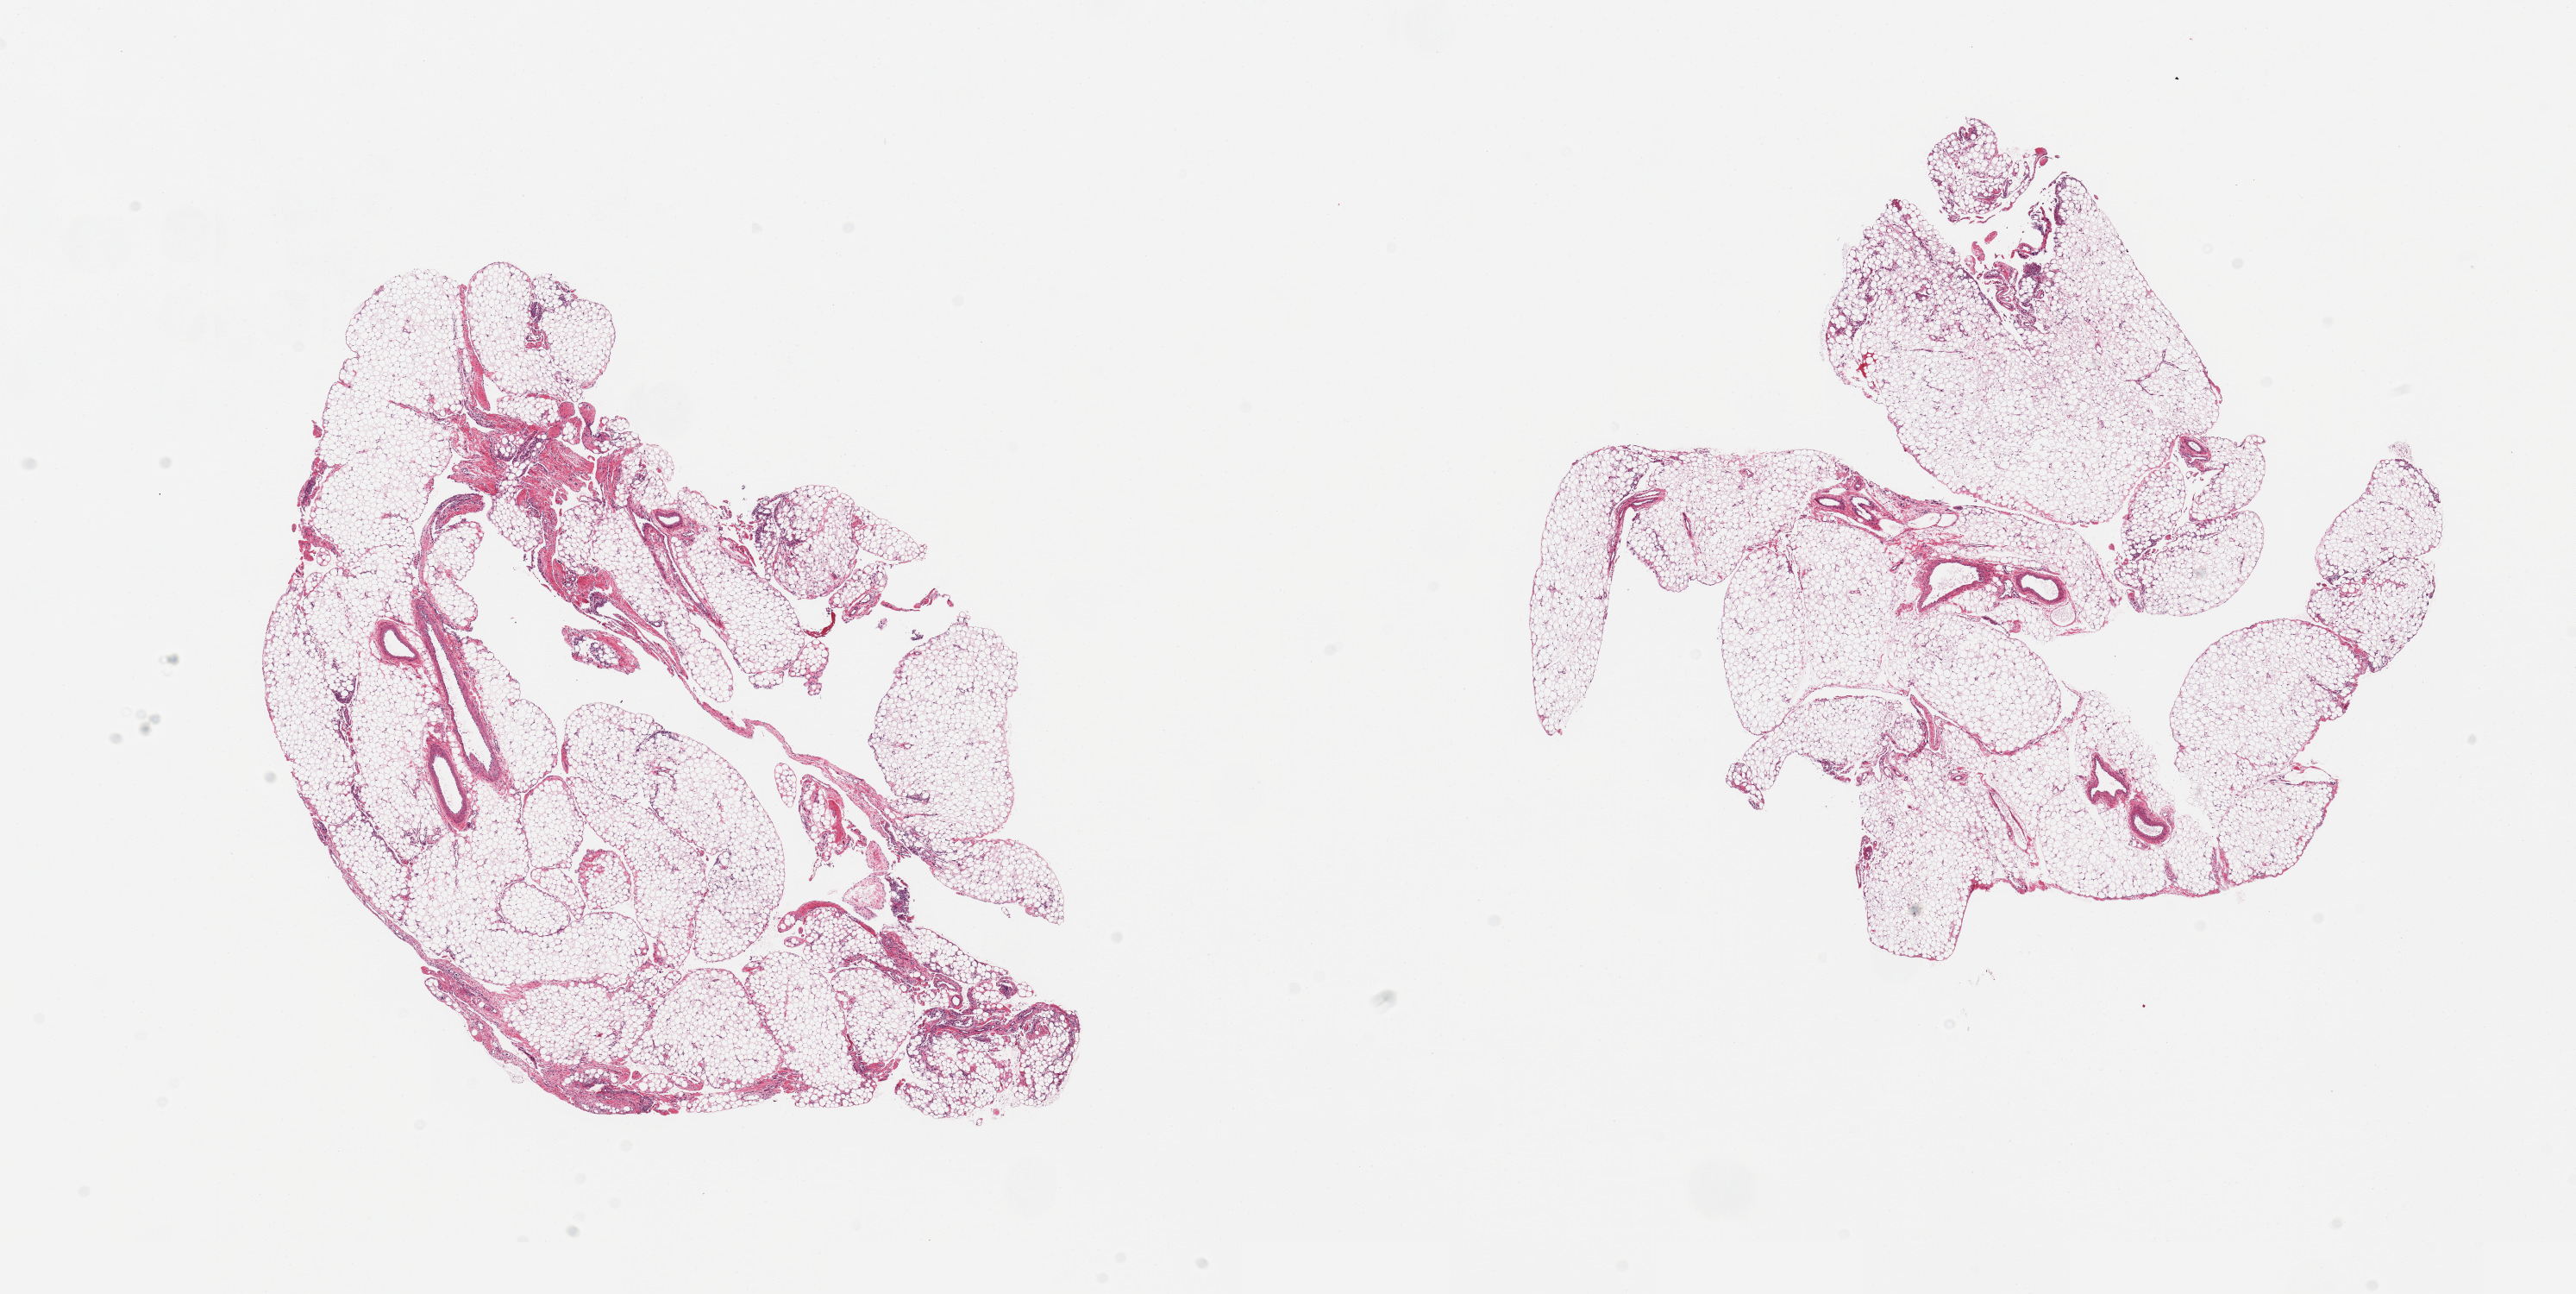
H&E whole-slide image, shown as a low-resolution overview of the whole scanned area (about 23.6 x 11.9 mm), PAXgene-fixed paraffin-embedded (PFPE) section, target tissue: omentum, tissue donor sample. Donor sex: female.
- pathologist's review note for this sample: 2 pieces